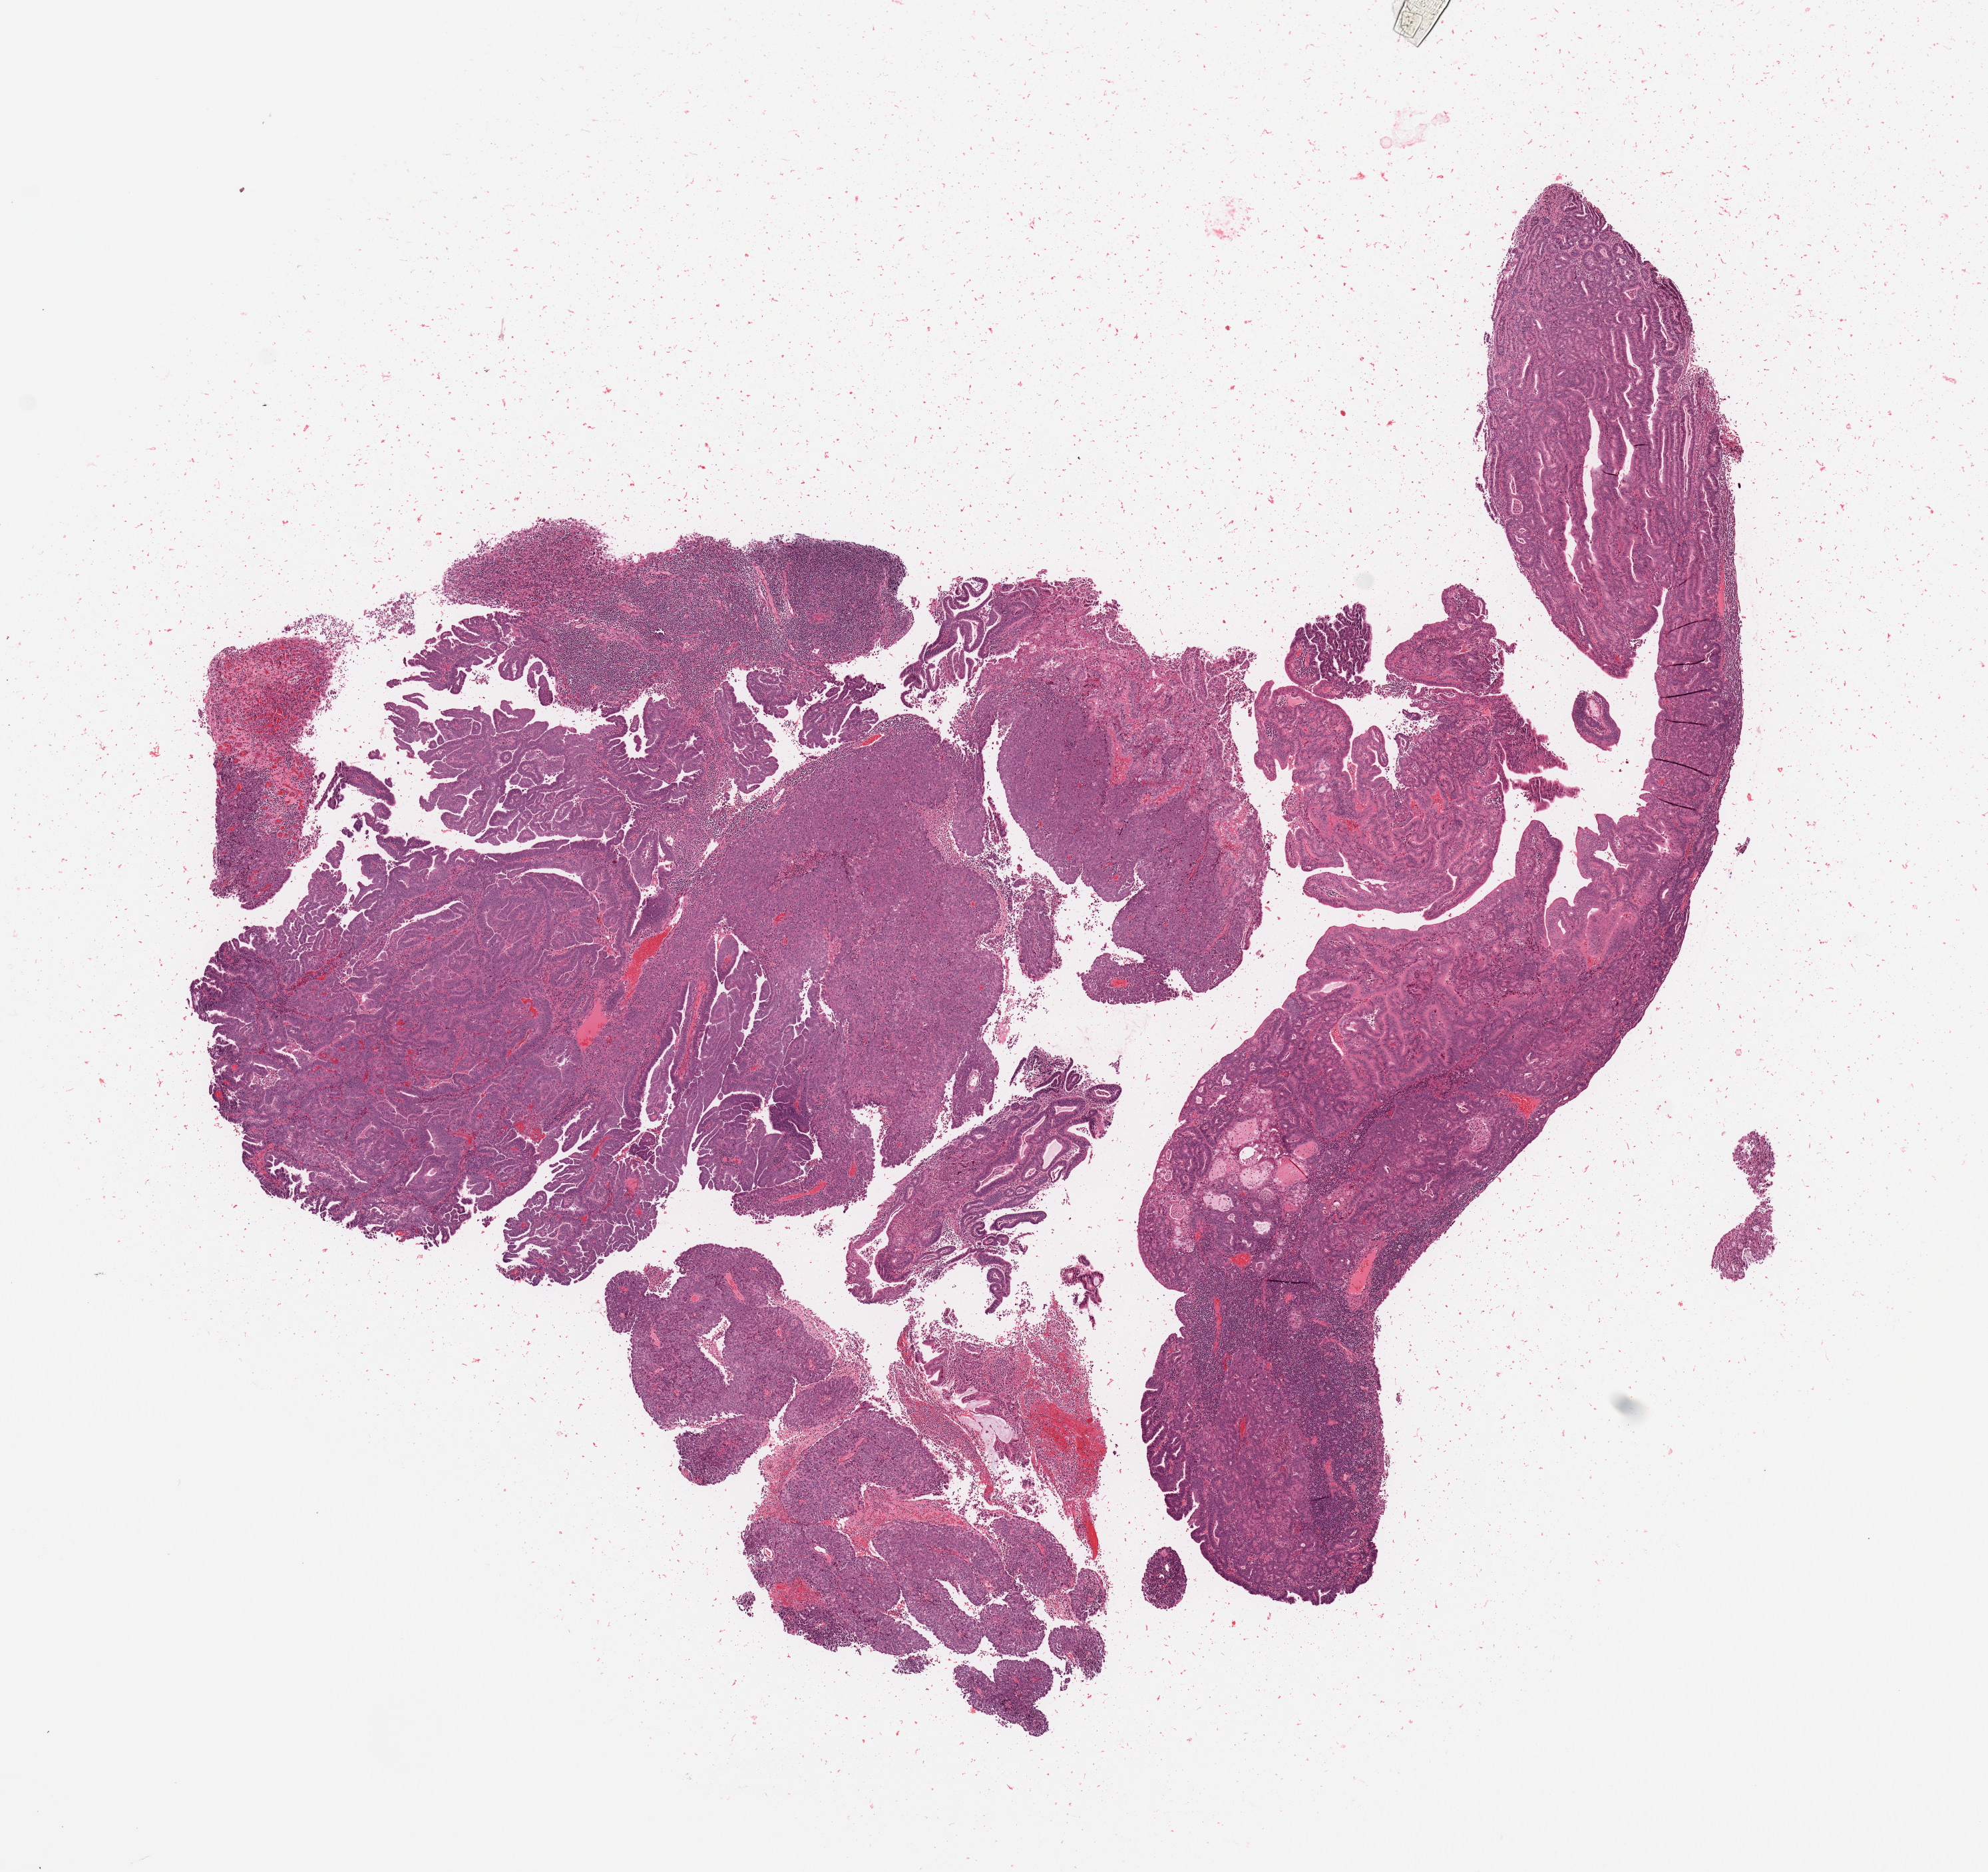
Hematoxylin and eosin (H&E) stained whole-slide image — low-resolution overview of the scanned area, about 11.8 x 11.1 mm (slide scanned at 20x). Tumour tissue sample, sampled site: uterus. 51-year-old female patient. Composition of this section per pathologist review: tumour nuclei 85%, necrosis 5%.
Histologic diagnosis: Endometrioid adenocarcinoma, NOS.